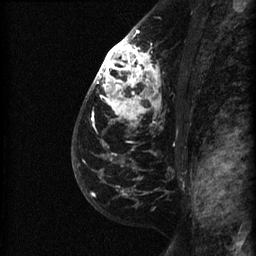
Breast MRI (dynamic contrast-enhanced), one sagittal slice; slice 44 of 60 in the series (ordered by position); dynamic contrast-enhanced series, image 2 of 3 at this slice position (ordered by acquisition); 1.5 T; TE 4.2 ms, TR 22.7 ms; 256 × 256 image matrix. Female patient, age 48 years. From the clinical record (not read from this slice): setting: breast cancer imaged before/during neoadjuvant chemotherapy; receptor status: triple-negative.
Outlined on this slice (semi-automatic segmentation, software-assisted and operator-edited):
- analysis volume of interest (the breast-tissue region the enhancement analysis was run in; not a lesion): bounding box <89,27,164,180> (left, top, right, bottom; pixels)
- tumour enhancement mask (voxels above the 90 % enhancement threshold inside the analysis volume of interest): <94,29,156,159>